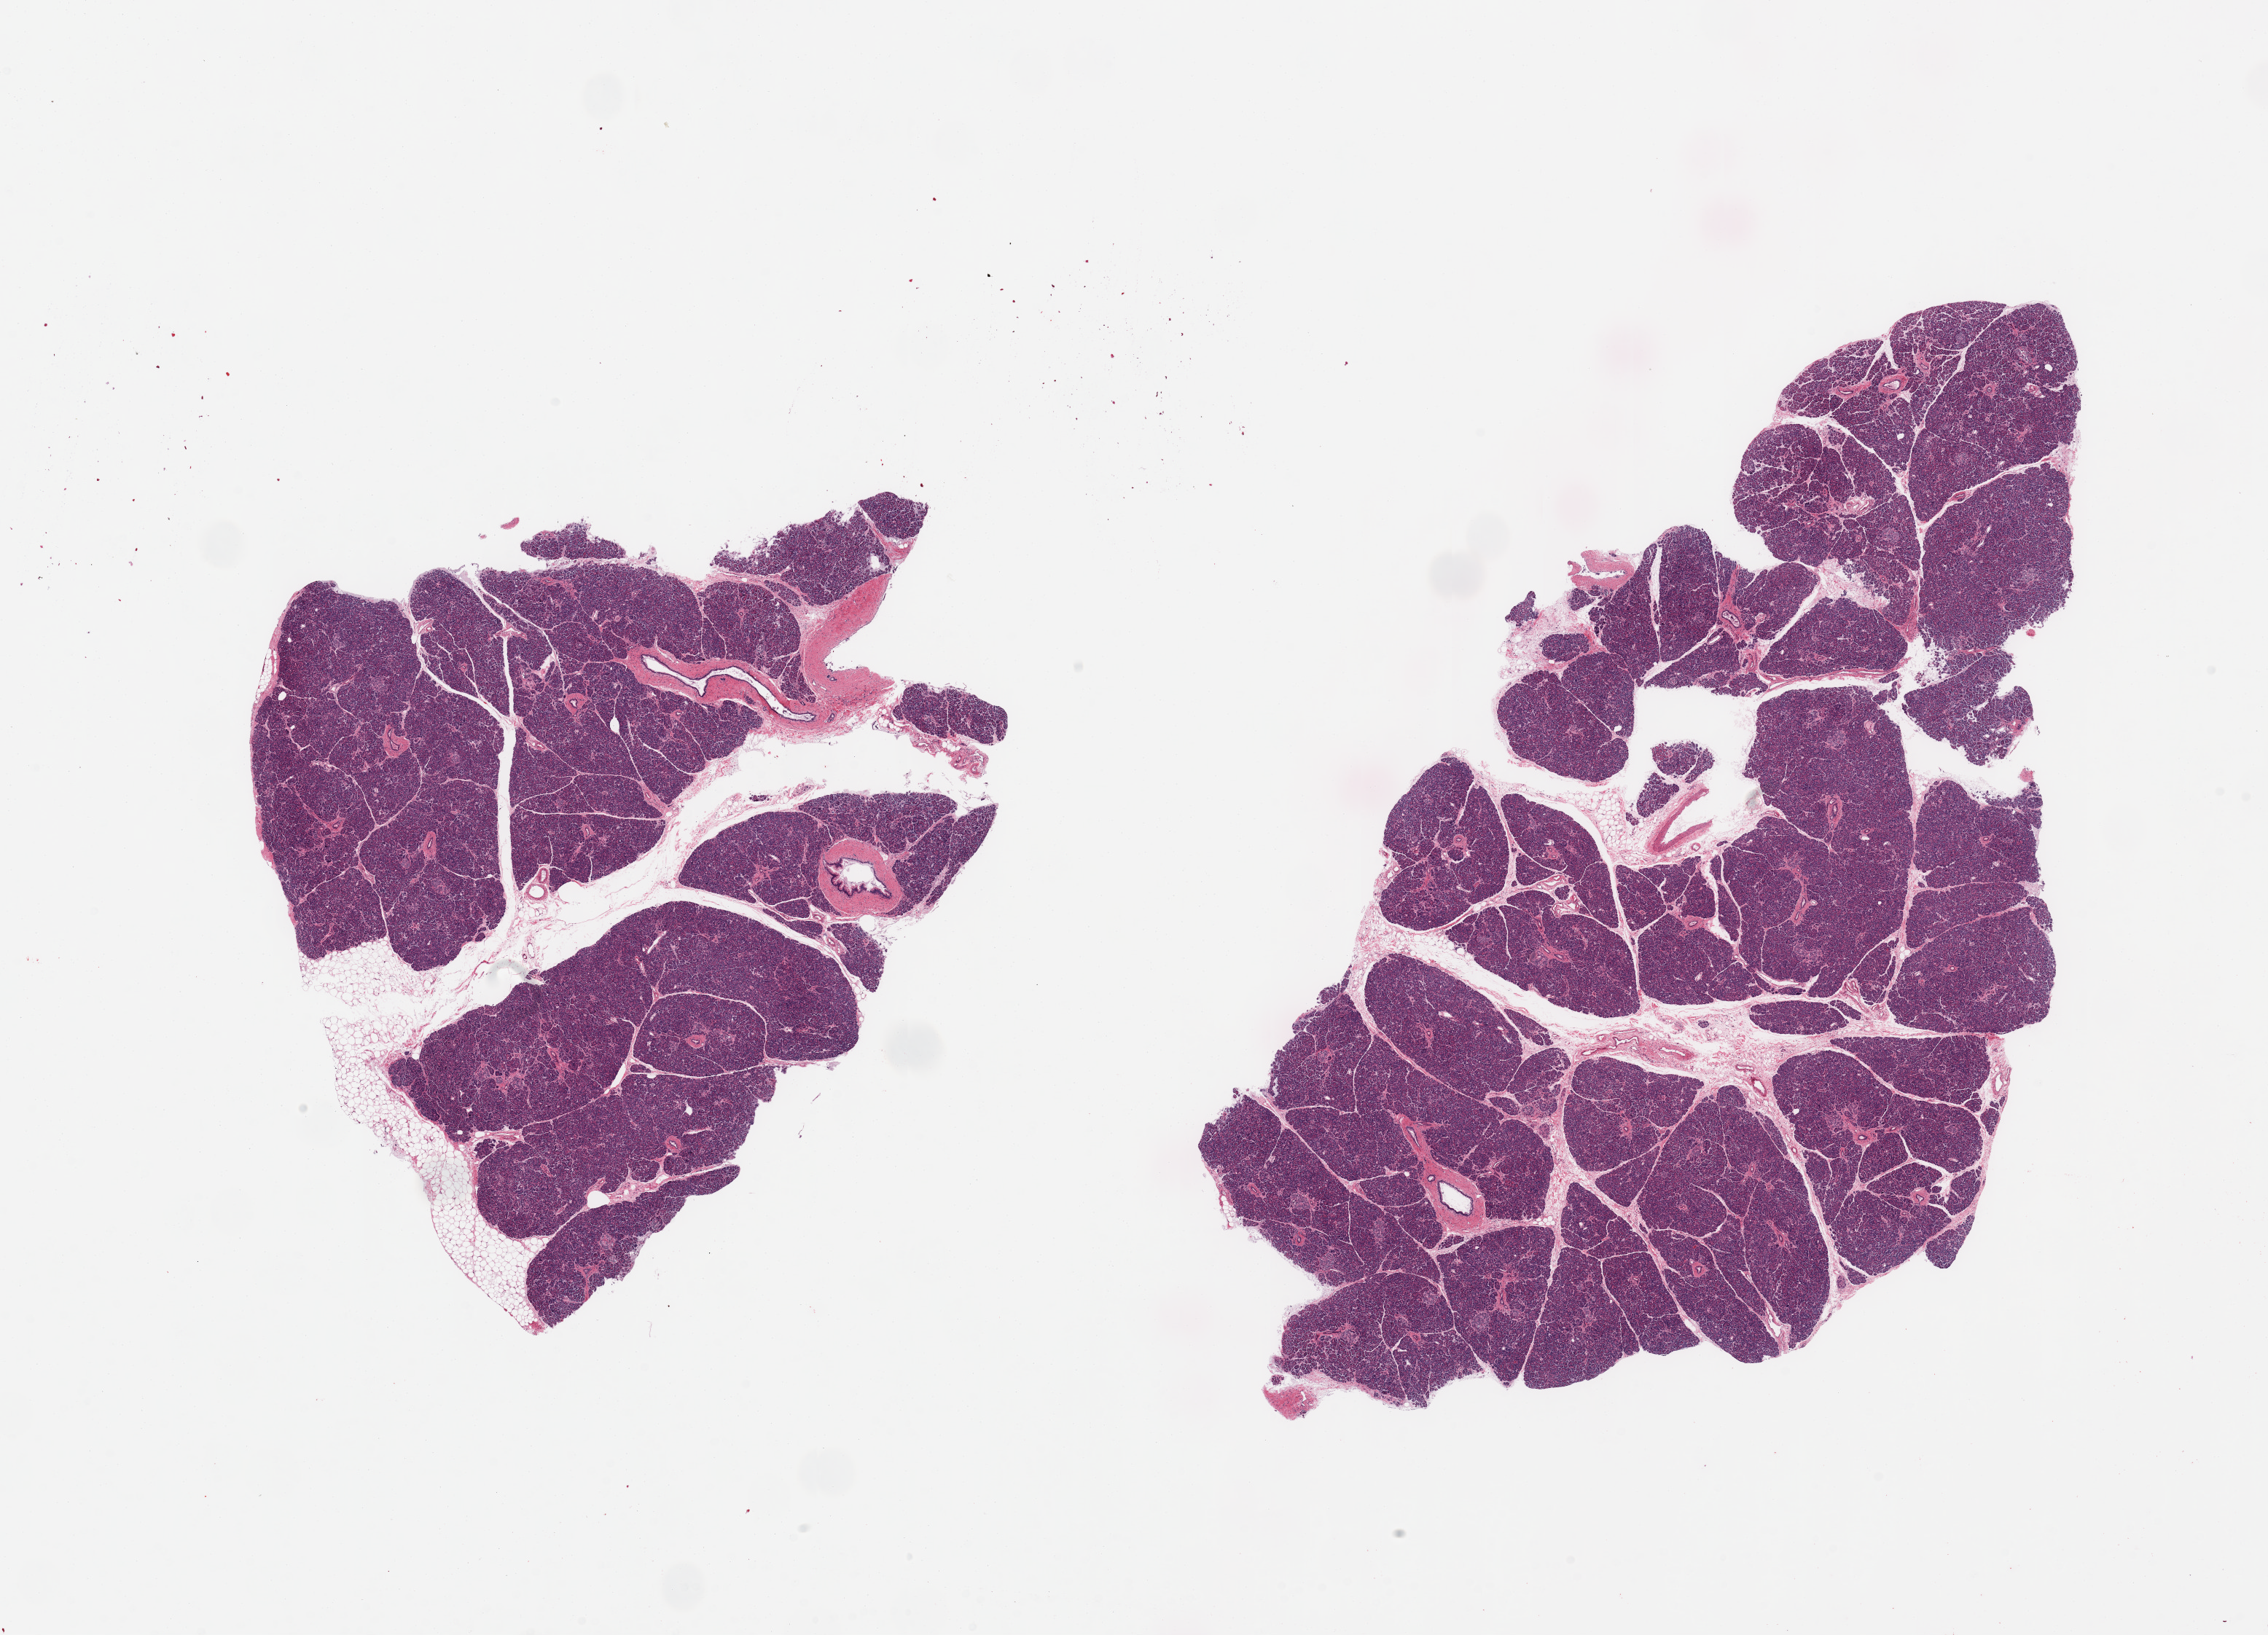
Whole-slide image, haematoxylin and eosin stain, brightfield, a low-resolution overview of the entire scanned area, about 24.6 x 17.7 mm (slide scanned at 20x); PAXgene-fixed paraffin-embedded (PFPE) section; target tissue: pancreas; donor tissue sample.
Reviewer comment on this tissue sample: 2 pieces; includes up to 10% attached and internal fat, islets well visualized, mild intralobular fibrosis, focal PanIN-1B.